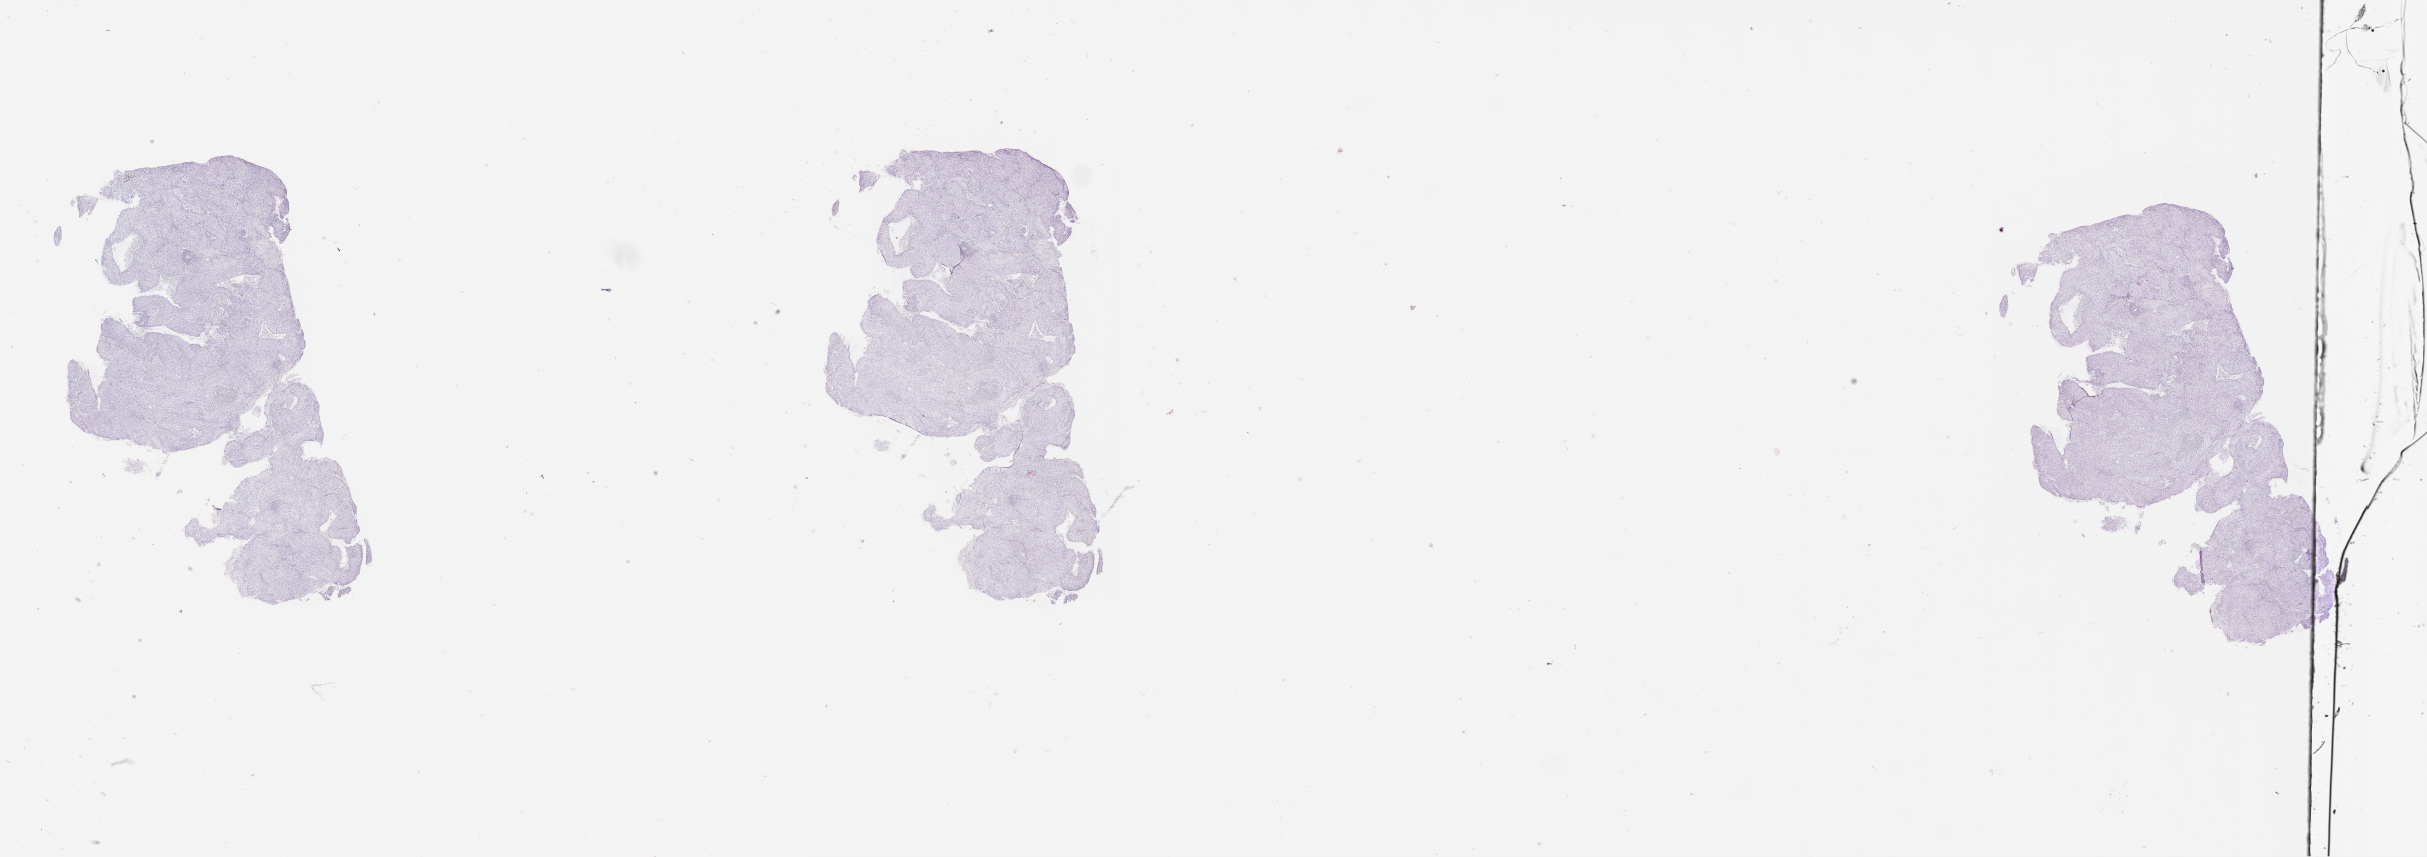
Hematoxylin and eosin (H&E) stained whole-slide image, whole scanned area (about 39.1 x 13.8 mm, from a 20x scan) shown as a low-resolution overview. Lung, tumour tissue. Patient: male, age 66 years.
Patient diagnosis (cohort enrolment): squamous cell carcinoma (lung).